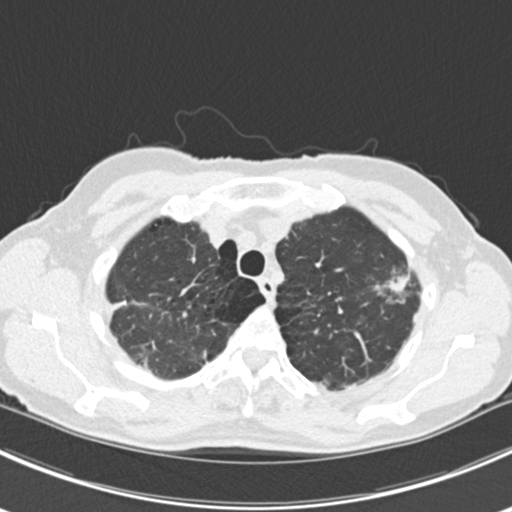
Chest CT (low-dose screening protocol), one axial image, baseline annual screen, lung window (W 1500 / L -600 HU), 120 kVp, 512 × 512 image matrix, field of view 310 × 310 mm. Female participant, aged 63 years at enrolment.
Expert reader's lesion annotation, bounding box (x1, y1, x2, y2) in pixels: (366, 257, 424, 316). The screening reader recorded 10 non-calcified nodules or masses ≥4 mm on this exam (right lower lobe, right lower lobe, left lower lobe, left lower lobe, right middle lobe, right lower lobe, left lower lobe, left upper lobe, right upper lobe, left upper lobe); which of them this box marks is not recorded. Official screen result: positive, change unspecified: nodule(s) >= 4 mm or enlarging nodule(s), mass(es), or other non-specific abnormalities suspicious for lung cancer. Participant outcome: lung cancer diagnosed 751 days after this screen — bronchiolo-alveolar adenocarcinoma, NOS, right upper lobe, right middle lobe, right lower lobe, left upper lobe, left lower lobe, moderately differentiated (G2), stage IV (AJCC 6th edition).